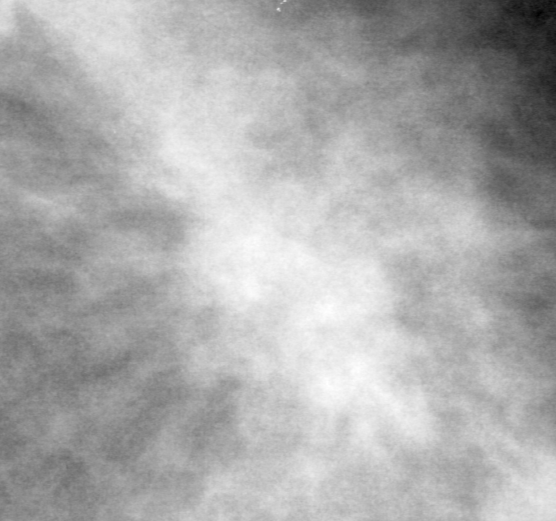
Crop from a digitized film mammogram around one marked abnormality, right breast, CC view.
Finding: mass, shape architectural distortion, margins ill defined; BI-RADS assessment category 4; subtlety rating 1 on a 1 (subtle) to 5 (obvious) scale; pathology result (as recorded, not read from the image): benign.